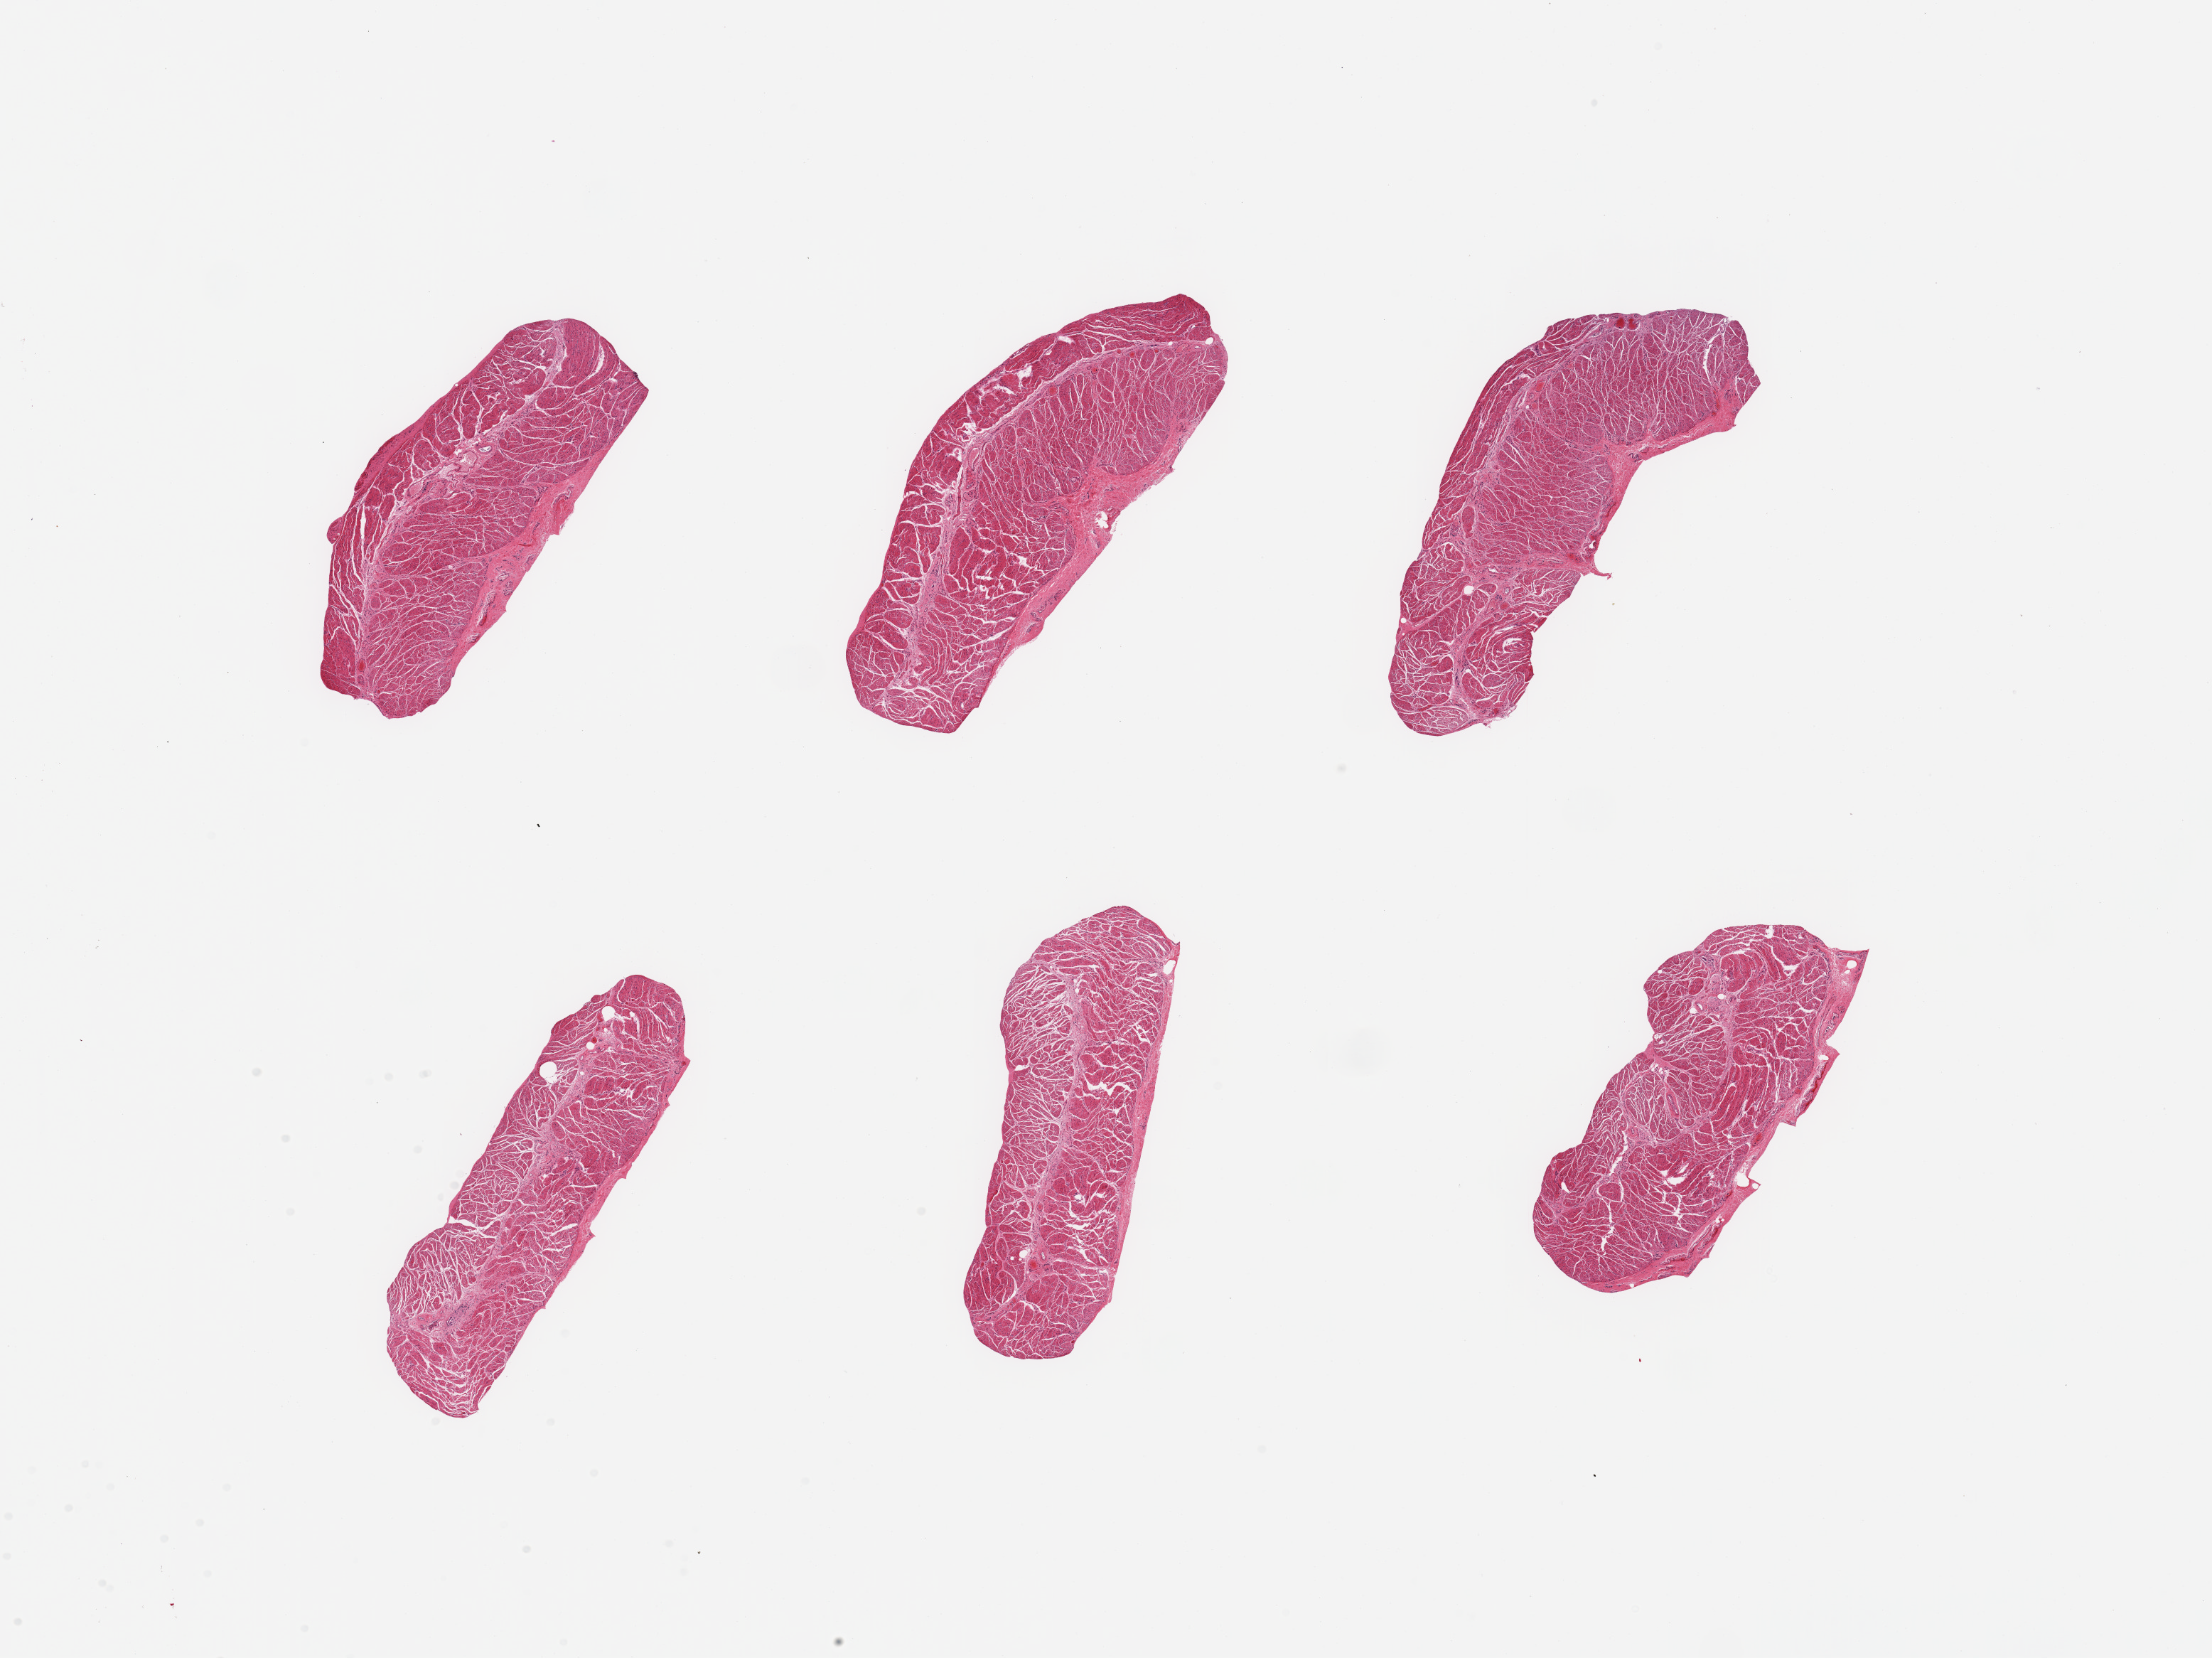
Haematoxylin and eosin whole-slide image, brightfield, low-resolution overview of the scanned area, about 24.6 x 18.4 mm (slide scanned at 20x), PAXgene-fixed paraffin-embedded (PFPE) section, target tissue: esophageal muscle, tissue donor sample. Male donor.
Pathologist's review note for this sample: 6 pieces, confirmed target muscularis.